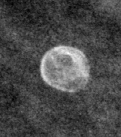
Crop from a digitized film mammogram around one marked abnormality; left breast; MLO view; BI-RADS breast density category 1 (scale 1–4).
Calcifications, morphology lucent centered; BI-RADS assessment category 2; benign without callback (not worked up further).